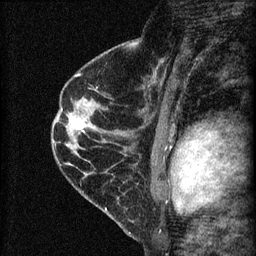
Breast MRI (dynamic contrast-enhanced), one sagittal slice; position 39 of 60 along the scan axis; dynamic contrast-enhanced series, image 2 of 4 at this slice position (ordered by acquisition); 1.5 T; TE 4.2 ms, TR 8.2 ms; 2 mm slice thickness; 256 × 256 image matrix, field of view 180 × 180 mm. Female patient, age 45 years.
Annotated regions visible in this slice (semi-automatically segmented with operator editing):
- analysis volume of interest (the breast-tissue region the enhancement analysis was run in; not a lesion): bounding box [x1, y1, x2, y2] px = [58, 107, 98, 147]
- tumour enhancement mask (voxels above the 70 % enhancement threshold inside the analysis volume of interest): [69, 119, 84, 129]